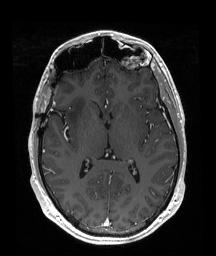
Brain MRI from a brain-tumour surgery series, one axial slice. Slice 102 of 192 in the series (ordered by position). T1-weighted post-contrast. 1 mm slice thickness. 216 × 256 image matrix. From the clinical record (not read from this slice): histopathology: Astrocytoma; WHO grade: 2; IDH mutation: yes.
Structures marked on this image (outlined manually by an expert reader):
- tumour: box from (x=67, y=97) to (x=86, y=128) px